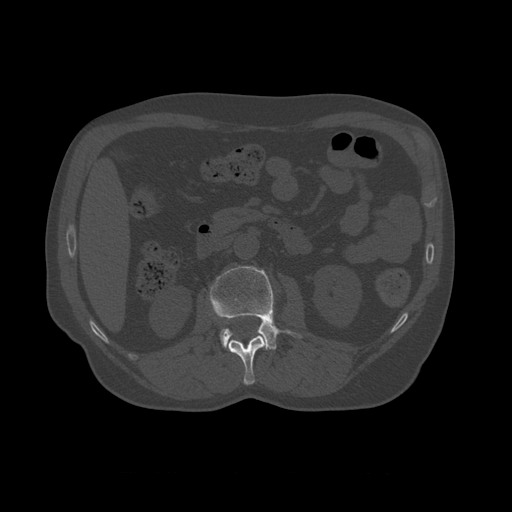
CT including the spine, one axial slice. Position 342 of 450 along the scan axis. Reconstruction kernel STANDARD. Bone window (W 1800 / L 400 HU). 512 × 512 image matrix, field of view 405 × 405 mm. Patient age 75 years. Case-level facts recorded for this patient, not image findings: primary cancer: prostate.
Structures marked on this image (semi-automatically segmented with operator editing):
- L1 vertebra: bounding box <228,336,268,385> (left, top, right, bottom; pixels)
- L2 vertebra: <209,266,302,351>